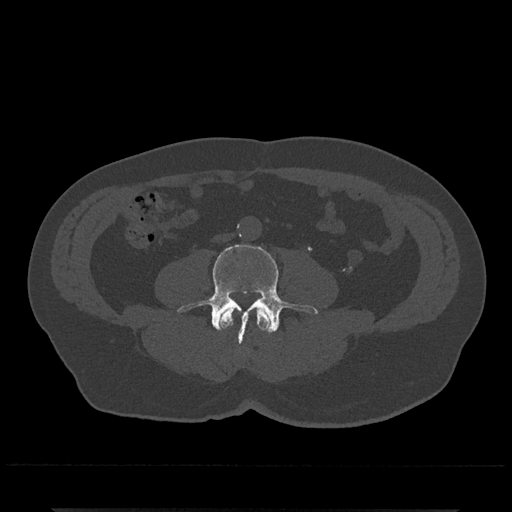
CT including the spine, one axial slice; slice 169 of 797 in the series (ordered by position); 120 kVp; bone window (W 1800 / L 400 HU); 0.5 mm slice thickness; 512 × 512 image matrix. Male patient, age 67 years. Case-level facts recorded for this patient, not image findings: primary cancer: prostate.
Outlined on this slice (semi-automatic segmentation, software-assisted and operator-edited):
- L3 vertebra: bounding box [x1, y1, x2, y2] px = [219, 307, 271, 333]
- L4 vertebra: [177, 244, 318, 343]